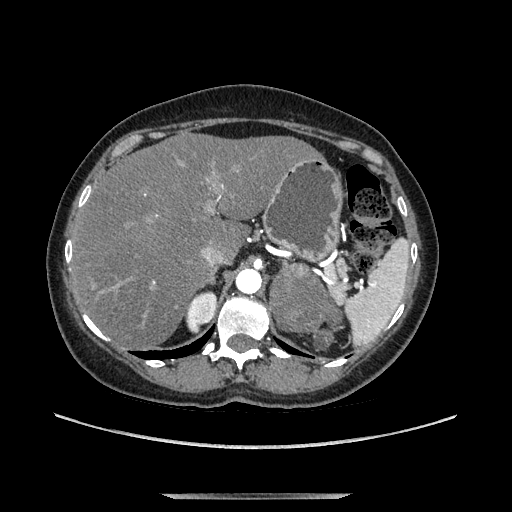
Contrast-enhanced abdominal CT, one axial slice. Position 92 of 169 along the scan axis. Soft-tissue window (W 400 / L 40 HU). 1.25 mm slice thickness. 512 × 512 image matrix. Female patient. From the clinical record (not read from this slice): diagnosis: adrenocortical carcinoma; tumour side: left adrenal; tumour size at pathology: 9 cm; Ki-67 index: 2 %.
Outlined on this slice (semi-automatic segmentation, software-assisted and operator-edited):
- mass: bounding box (x1, y1, x2, y2) in pixels: (272, 265, 339, 348)